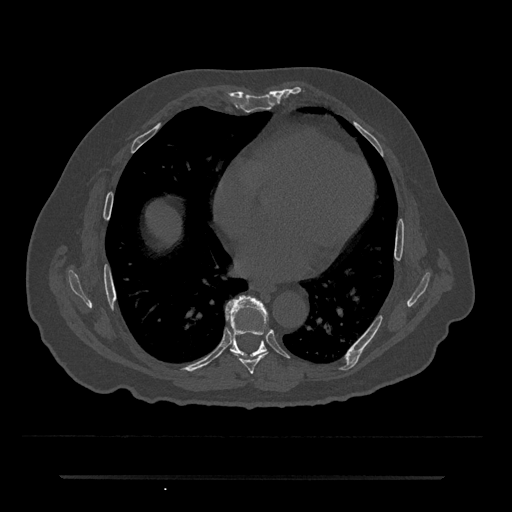
CT including the spine, one axial slice; slice 361 of 797 in the series (ordered by position); 120 kVp; bone window (W 1800 / L 400 HU); 0.5 mm slice thickness; 512 × 512 image matrix, field of view 437 × 437 mm. Male patient, age 69 years. From the clinical record (not read from this slice): primary cancer: prostate.
Outlined on this slice (semi-automatically segmented with operator editing):
- T7 vertebra: bounding box (x1, y1, x2, y2) in pixels: (232, 351, 268, 374)
- T8 vertebra: (226, 295, 267, 357)